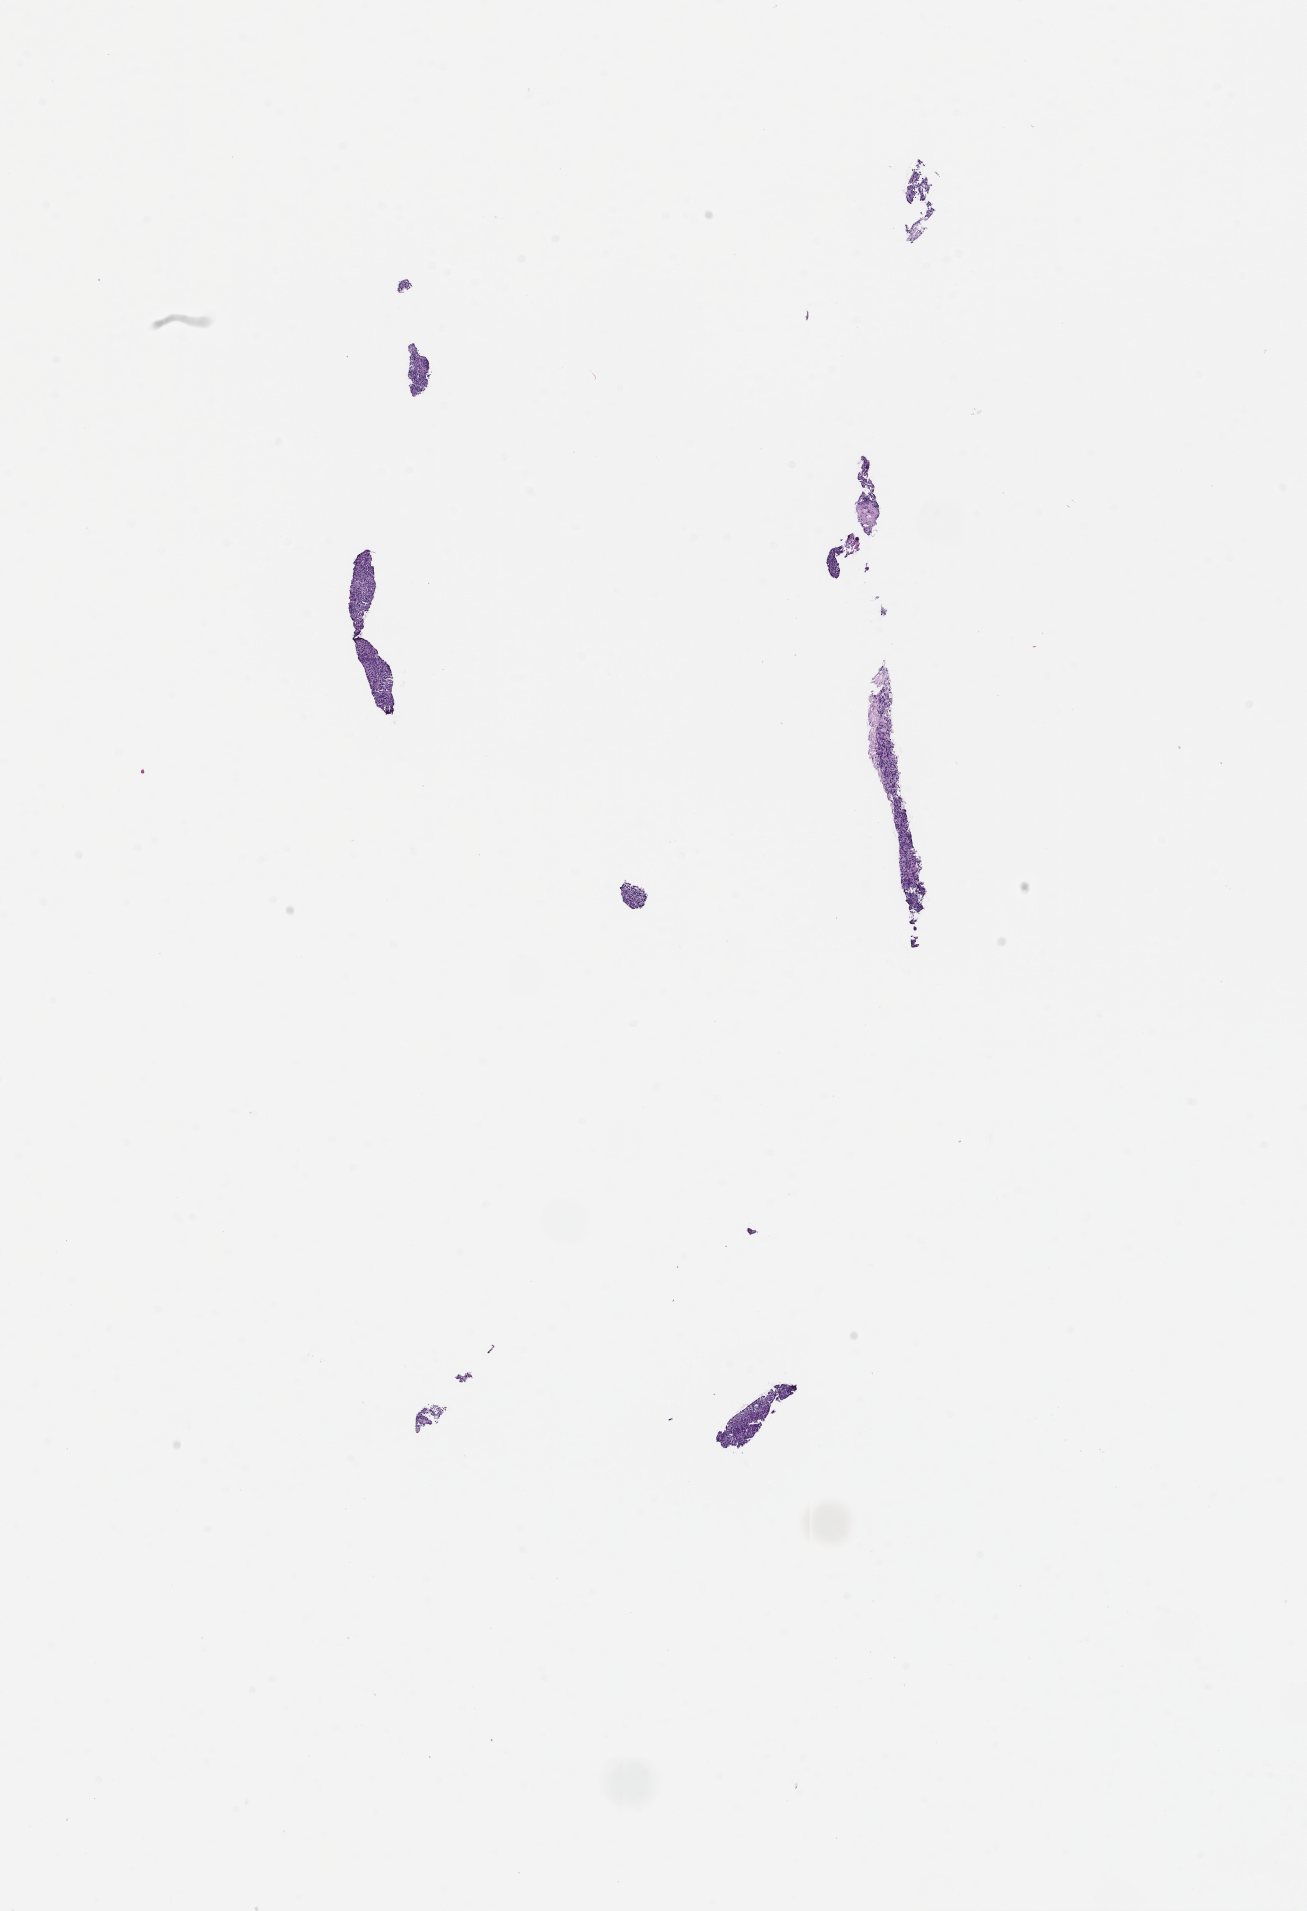
Whole-slide image, haematoxylin and eosin stain — whole scanned area (about 10.6 x 15.4 mm) shown as a low-resolution overview; FFPE section; archival tissue. Patient: male.
This section: metastasis (sampled organ not recorded). Primary diagnosis of the patient: Melanoma.